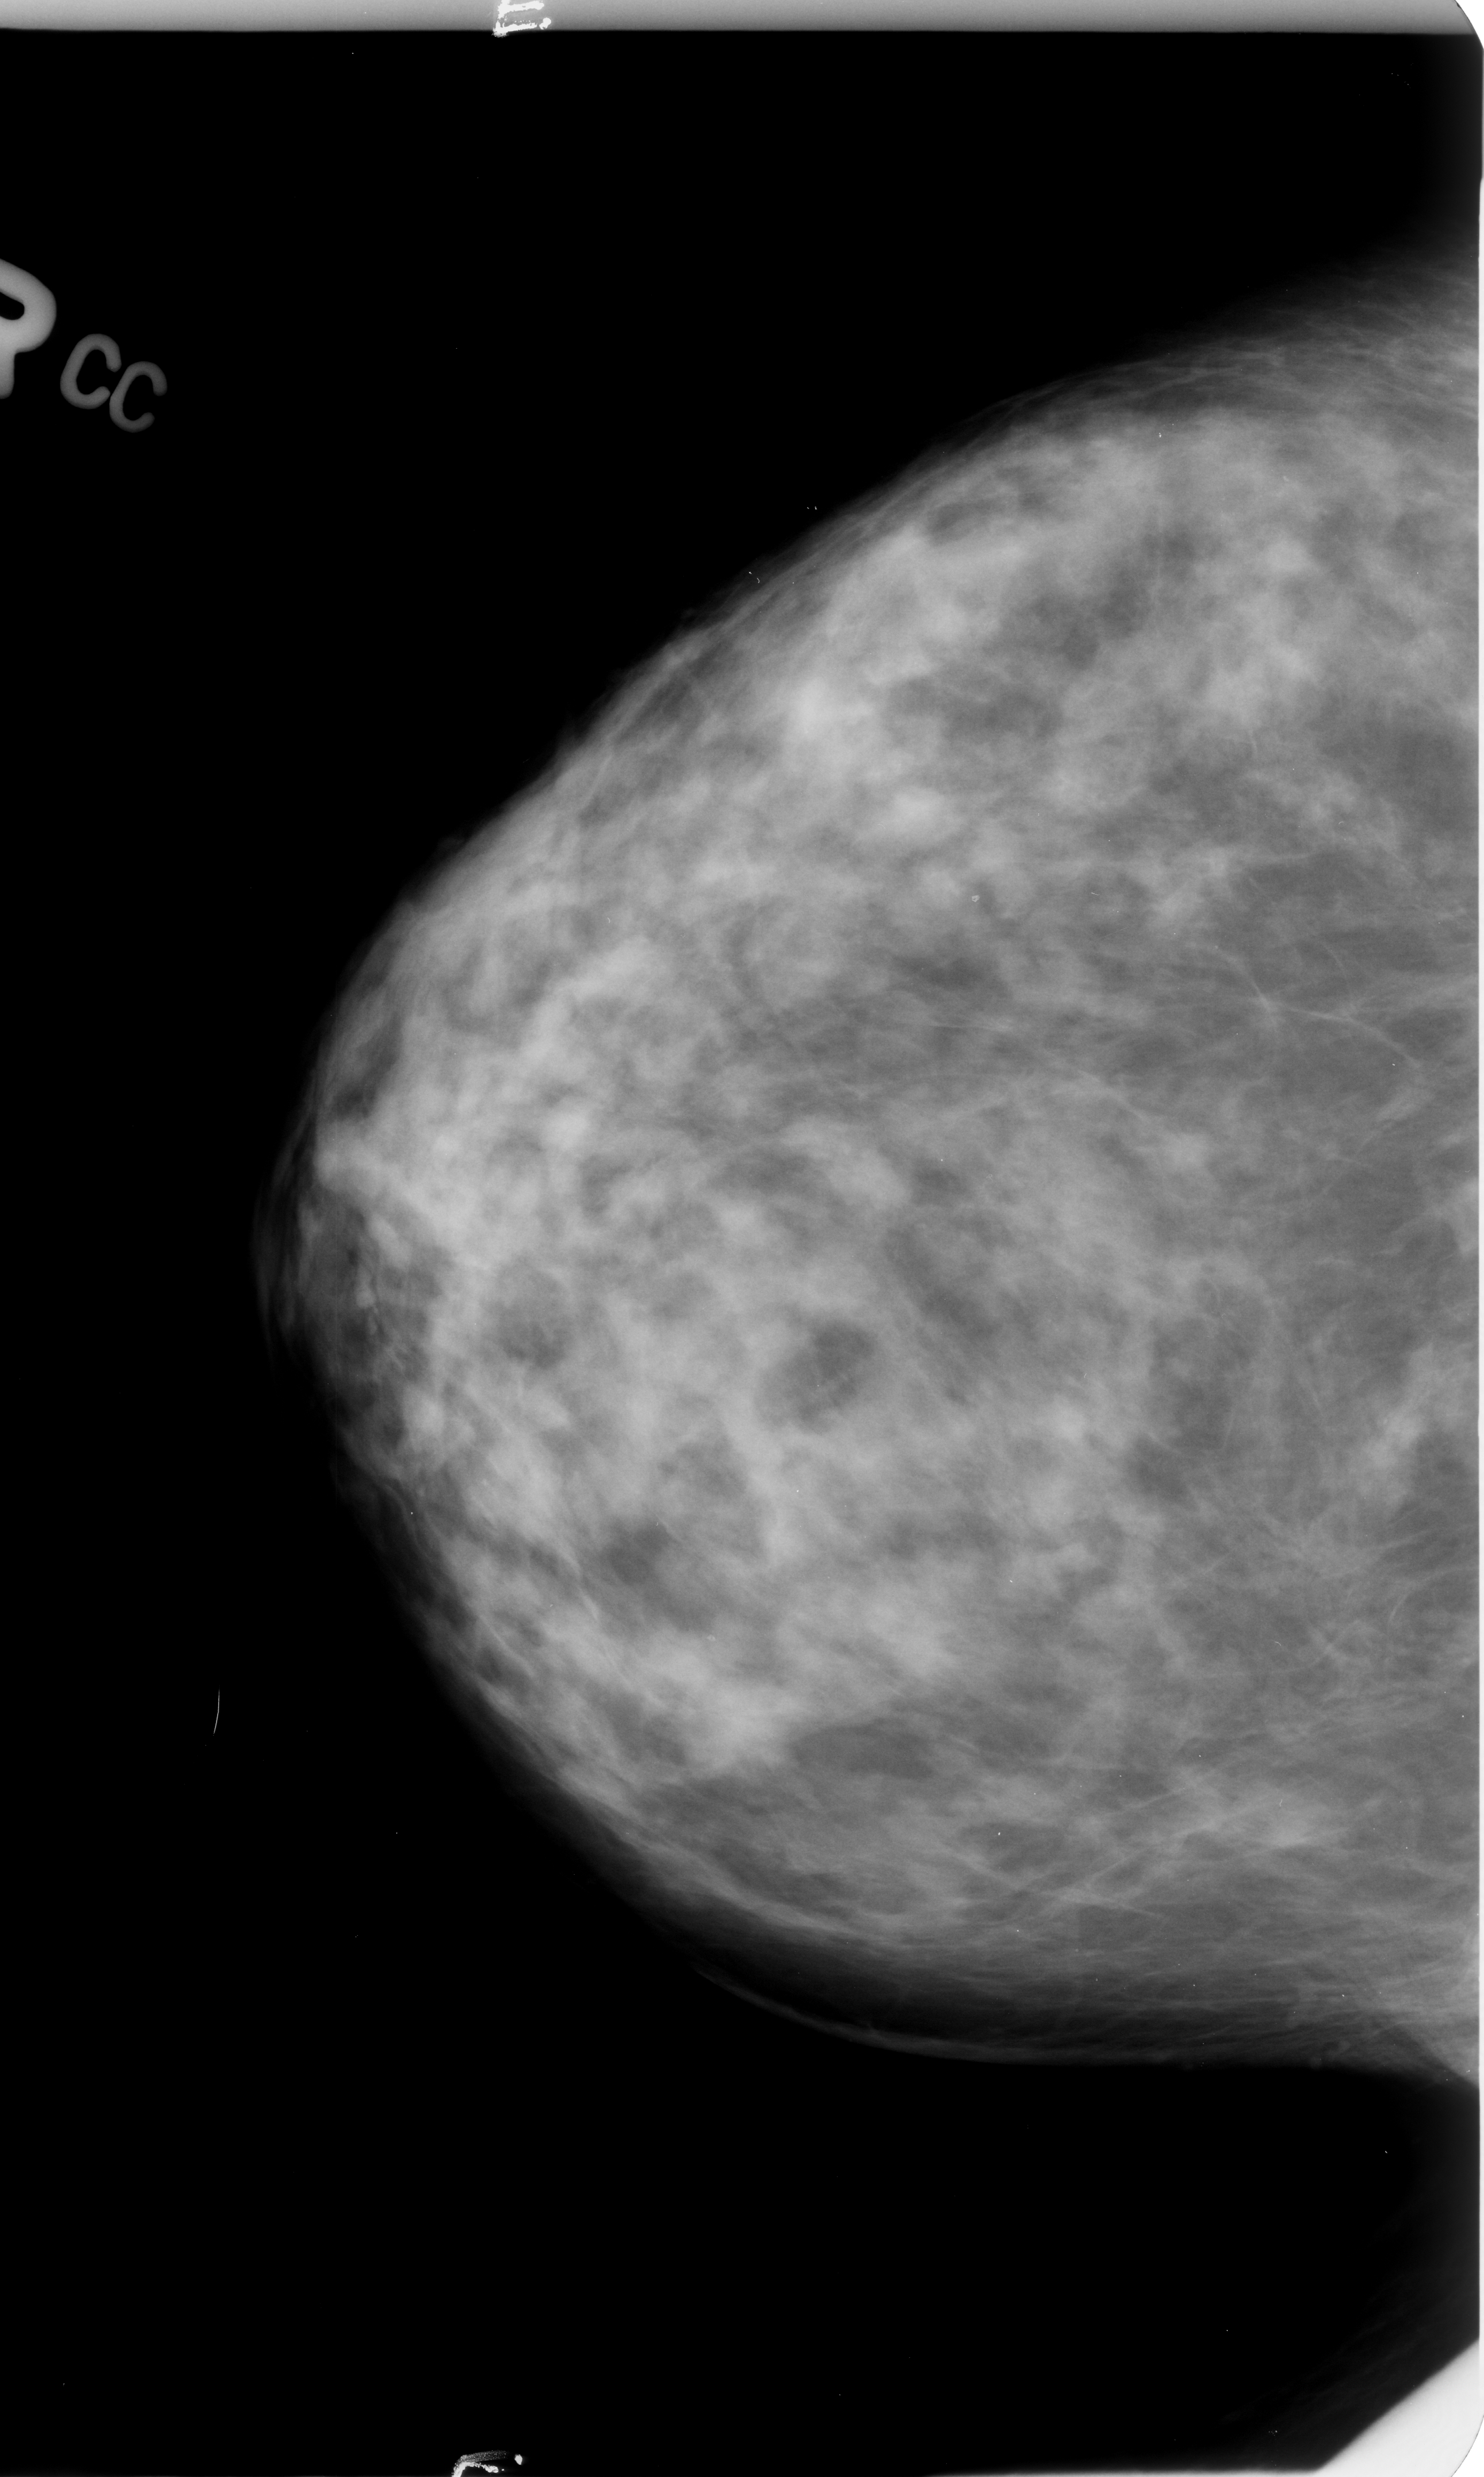
Scanned film-screen mammogram; right breast; CC view; breast composition: heterogeneously dense (BI-RADS density category 3 of 4).
Marked abnormality: calcifications, morphology pleomorphic, distribution clustered; BI-RADS assessment category 4; subtlety rating 2 on a 1 (subtle) to 5 (obvious) scale; pathology result (as recorded, not read from the image): benign.